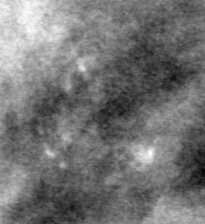
Crop from a digitized film mammogram around one marked abnormality, left breast, MLO view, BI-RADS breast density category 4 (scale 1–4).
Marked abnormality: calcifications, morphology pleomorphic, distribution clustered; BI-RADS assessment category 4; subtlety rating 3 on a 1 (subtle) to 5 (obvious) scale; pathology (as recorded): malignant.